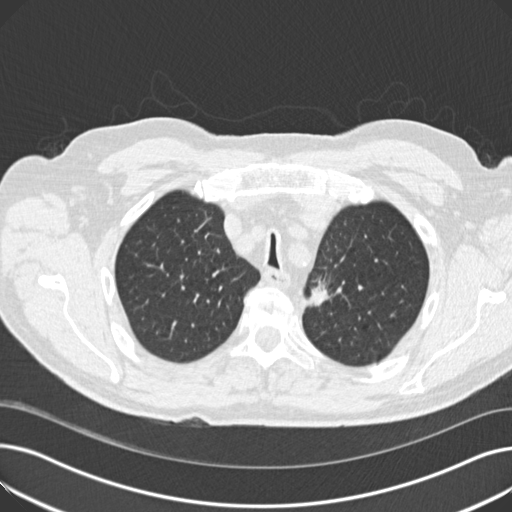
Low-dose screening chest CT, one axial slice; position 147 of 191 along the scan axis; 120 kVp; lung window (W 1500 / L -600 HU); 2 mm slice thickness; 512 × 512 image matrix, field of view 370 × 370 mm.
Annotated regions visible in this slice (expert manual segmentation):
- lesion 1 (tumor, upper lobe of left lung): box from (x=309, y=280) to (x=329, y=306) px